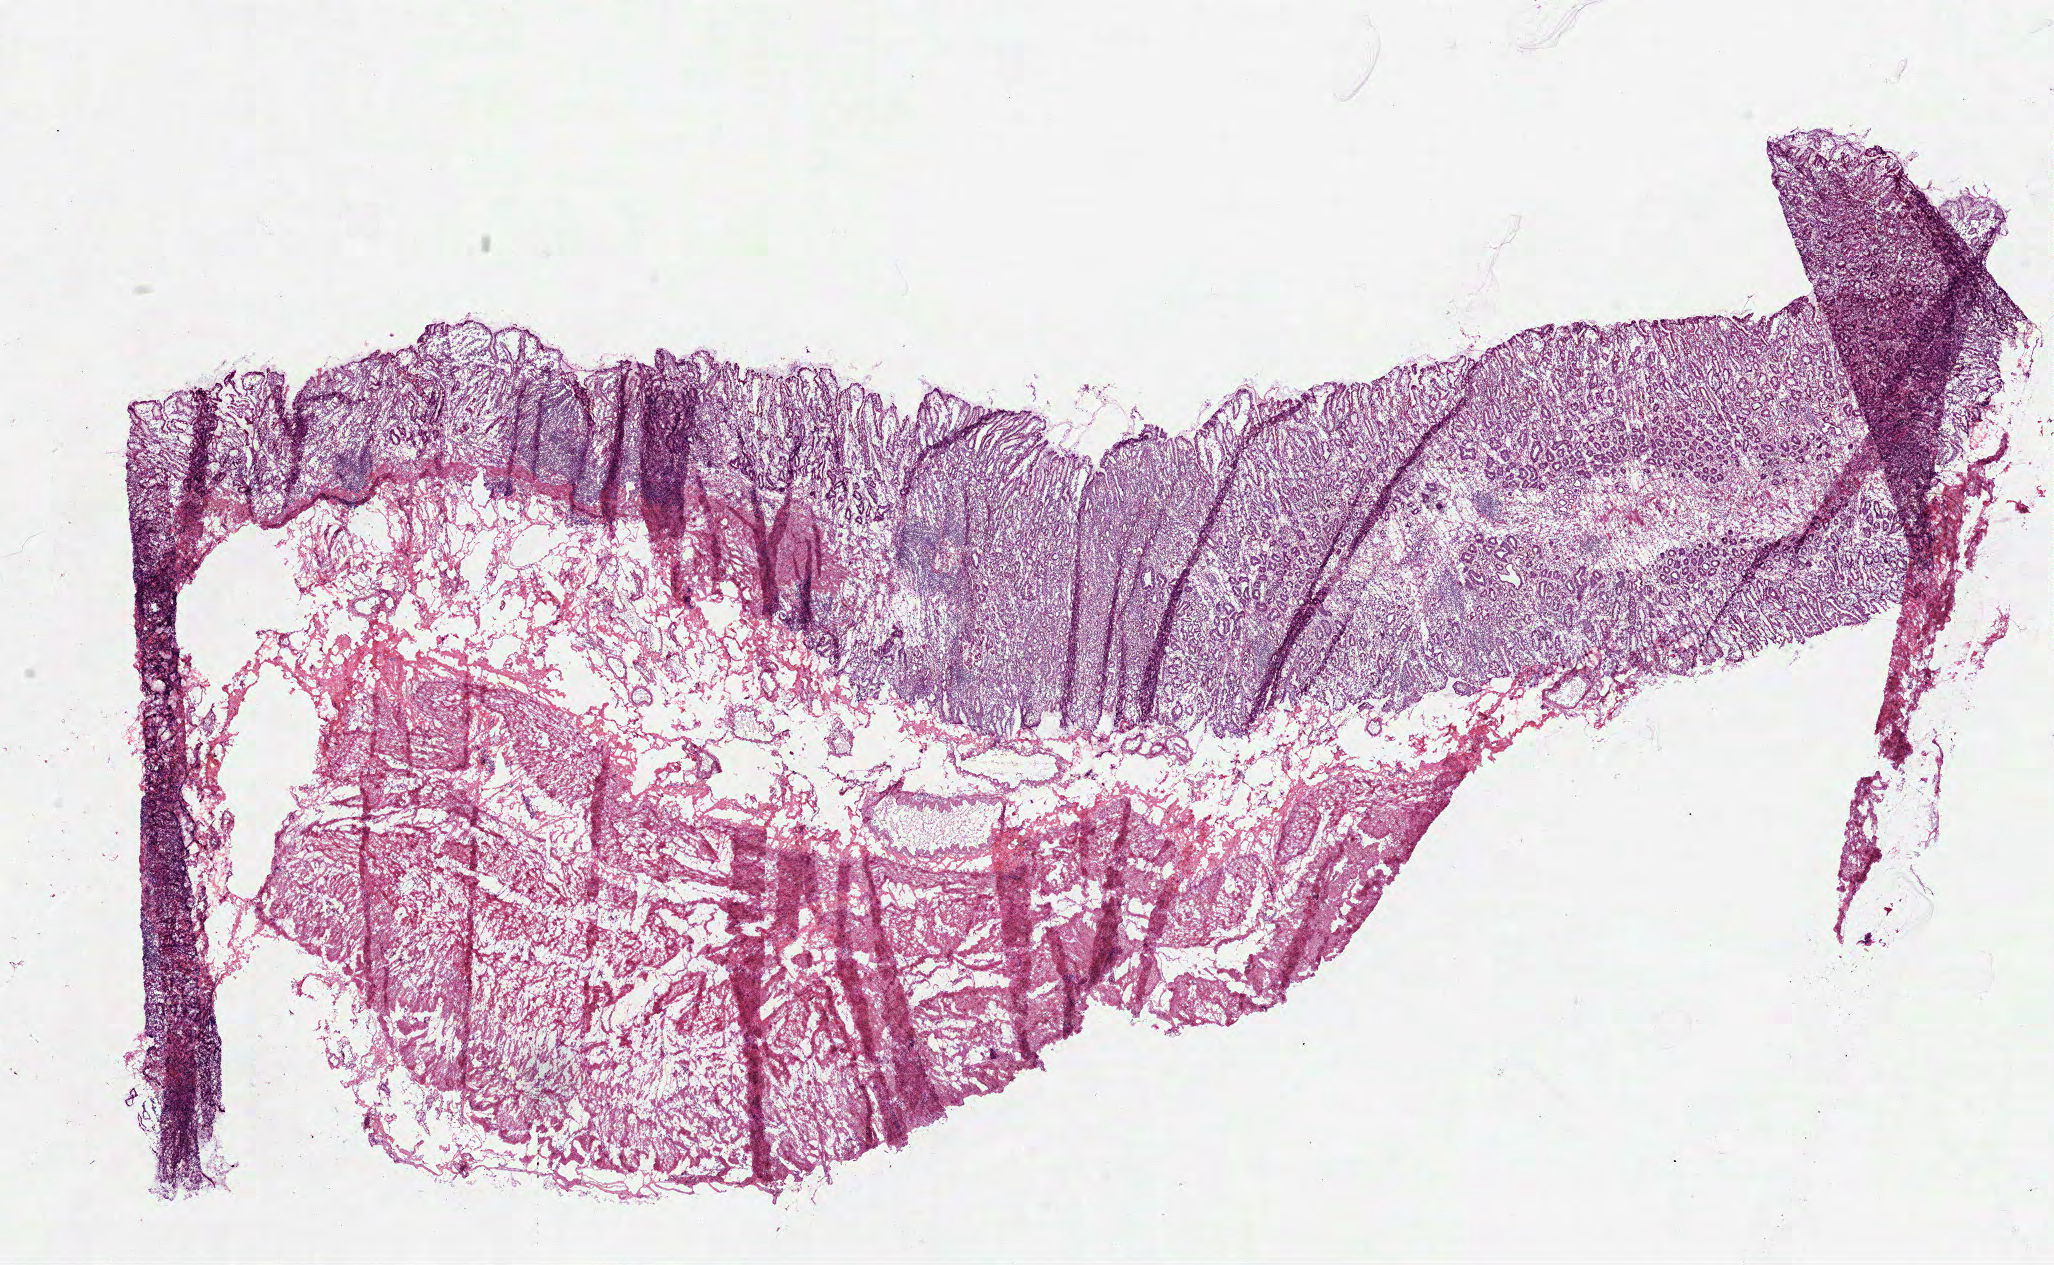
H&E whole-slide image — a low-resolution overview of the entire scanned area, about 16.6 x 10.2 mm (from a 40x scan), frozen section from the top of the tissue portion, stomach, solid tissue normal (non-tumour tissue) sample. Male patient; age at initial diagnosis 54 years.
This section: solid tissue normal sample (biorepository sample class). Patient diagnosis: Adenocarcinoma, NOS (body of stomach).